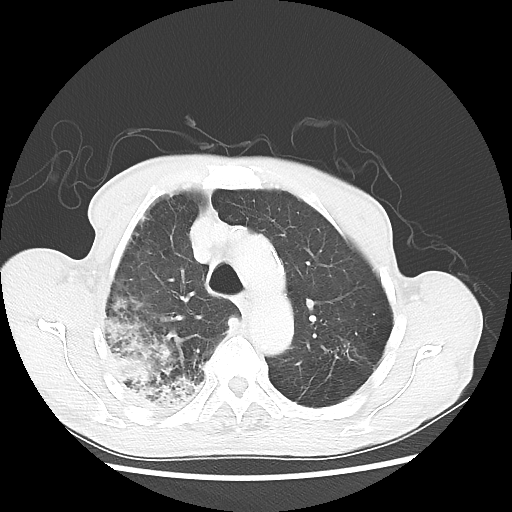
Chest CT, one axial slice. Position 41 of 58 along the scan axis. Reconstruction kernel LUNG. Lung window (W 1500 / L -600 HU). 5 mm slice thickness. 512 × 512 image matrix, field of view 351 × 351 mm. Male patient, age 75 years. From the clinical record (not read from this slice): clinical TNM (as recorded): T4 N1 M1.
Annotated regions visible in this slice (rectangle marked by the reading radiologist):
- lung tumour (recorded histology: adenocarcinoma): bounding box [x1, y1, x2, y2] px = [89, 290, 201, 407]